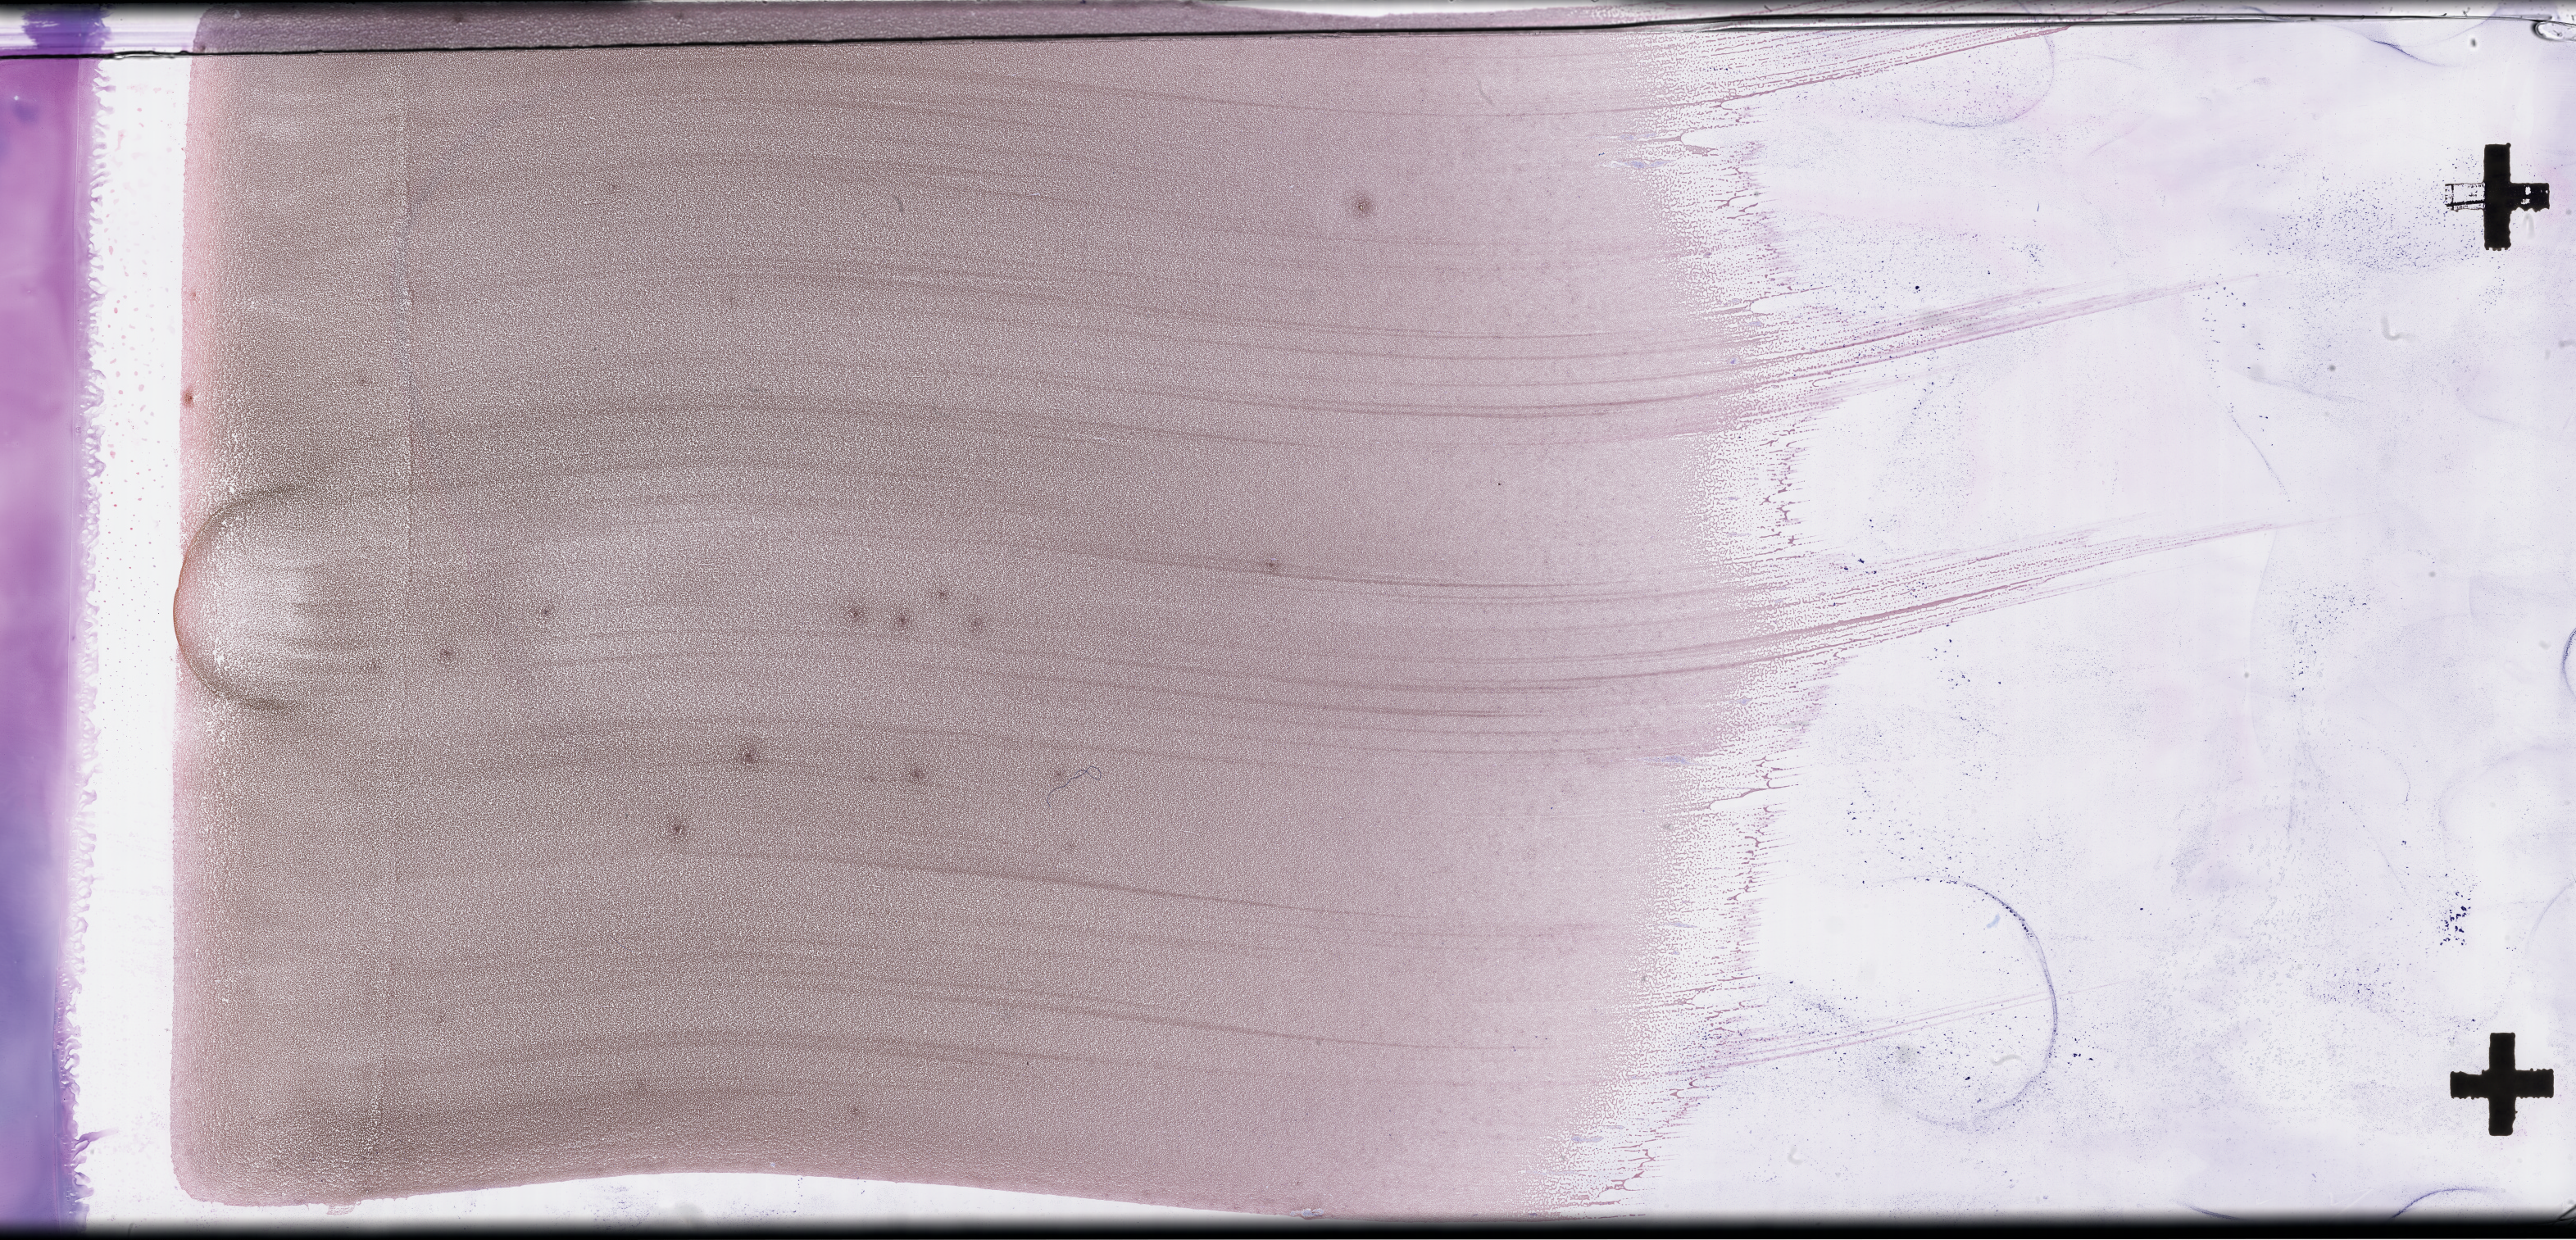
Whole-slide image of a whole blood smear, Wright–Giemsa stain, a low-resolution overview of the entire scanned area, about 50.8 x 24.4 mm; collected at baseline (before treatment). Patient sex: male.
* patient diagnosis: Plasma Cell Myeloma